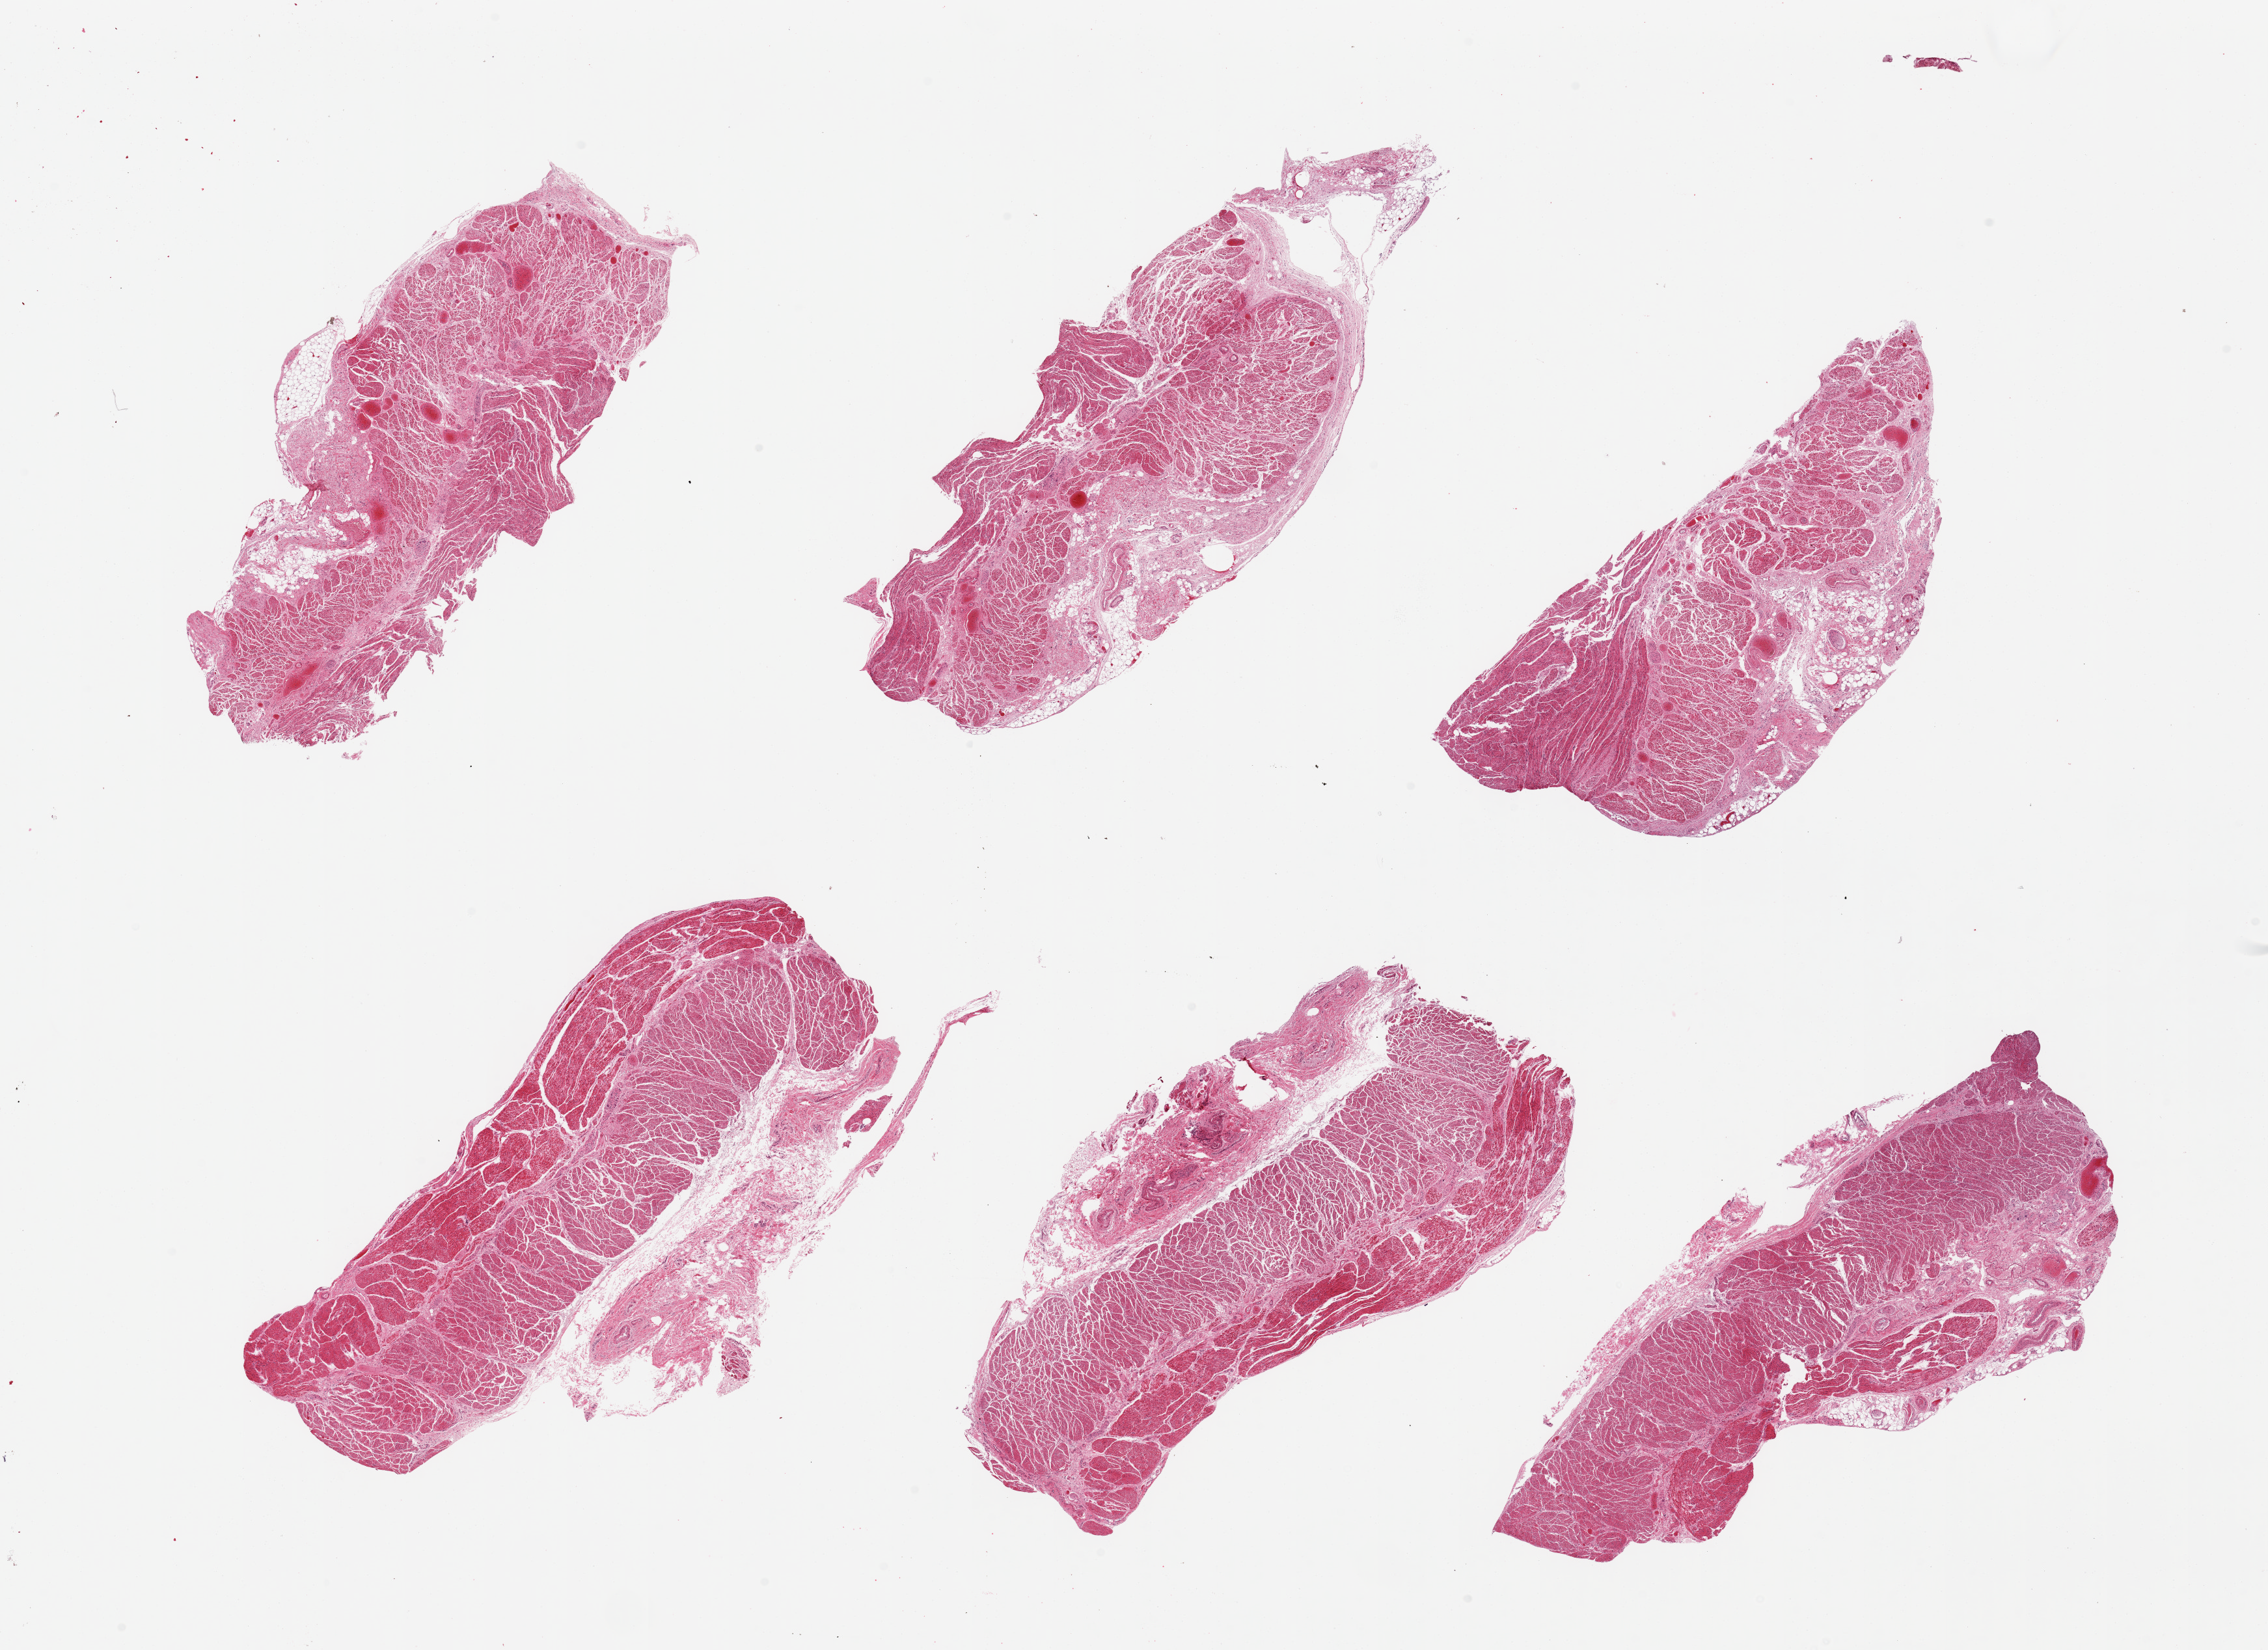
Hematoxylin and eosin (H&E) whole-slide image, brightfield, shown as a low-resolution overview of the whole scanned area (about 27.6 x 20.1 mm, slide scanned at 20x); PAXgene-fixed paraffin-embedded (PFPE) section; sampled site (target tissue): gastroesophageal junction; donor tissue sample. Female donor.
Review note (as recorded): 6 pieces; target muscularis with some attached submucosa/adventitia.